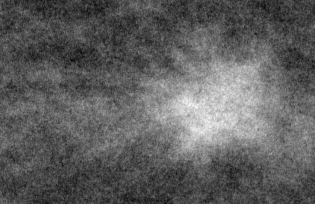
Region of interest cut from a scanned film mammogram (one marked finding), left breast, CC view, BI-RADS breast density category 2 (scale 1–4).
Finding: mass, shape irregular, margins spiculated; BI-RADS assessment category 4; pathology result (as recorded, not read from the image): malignant.